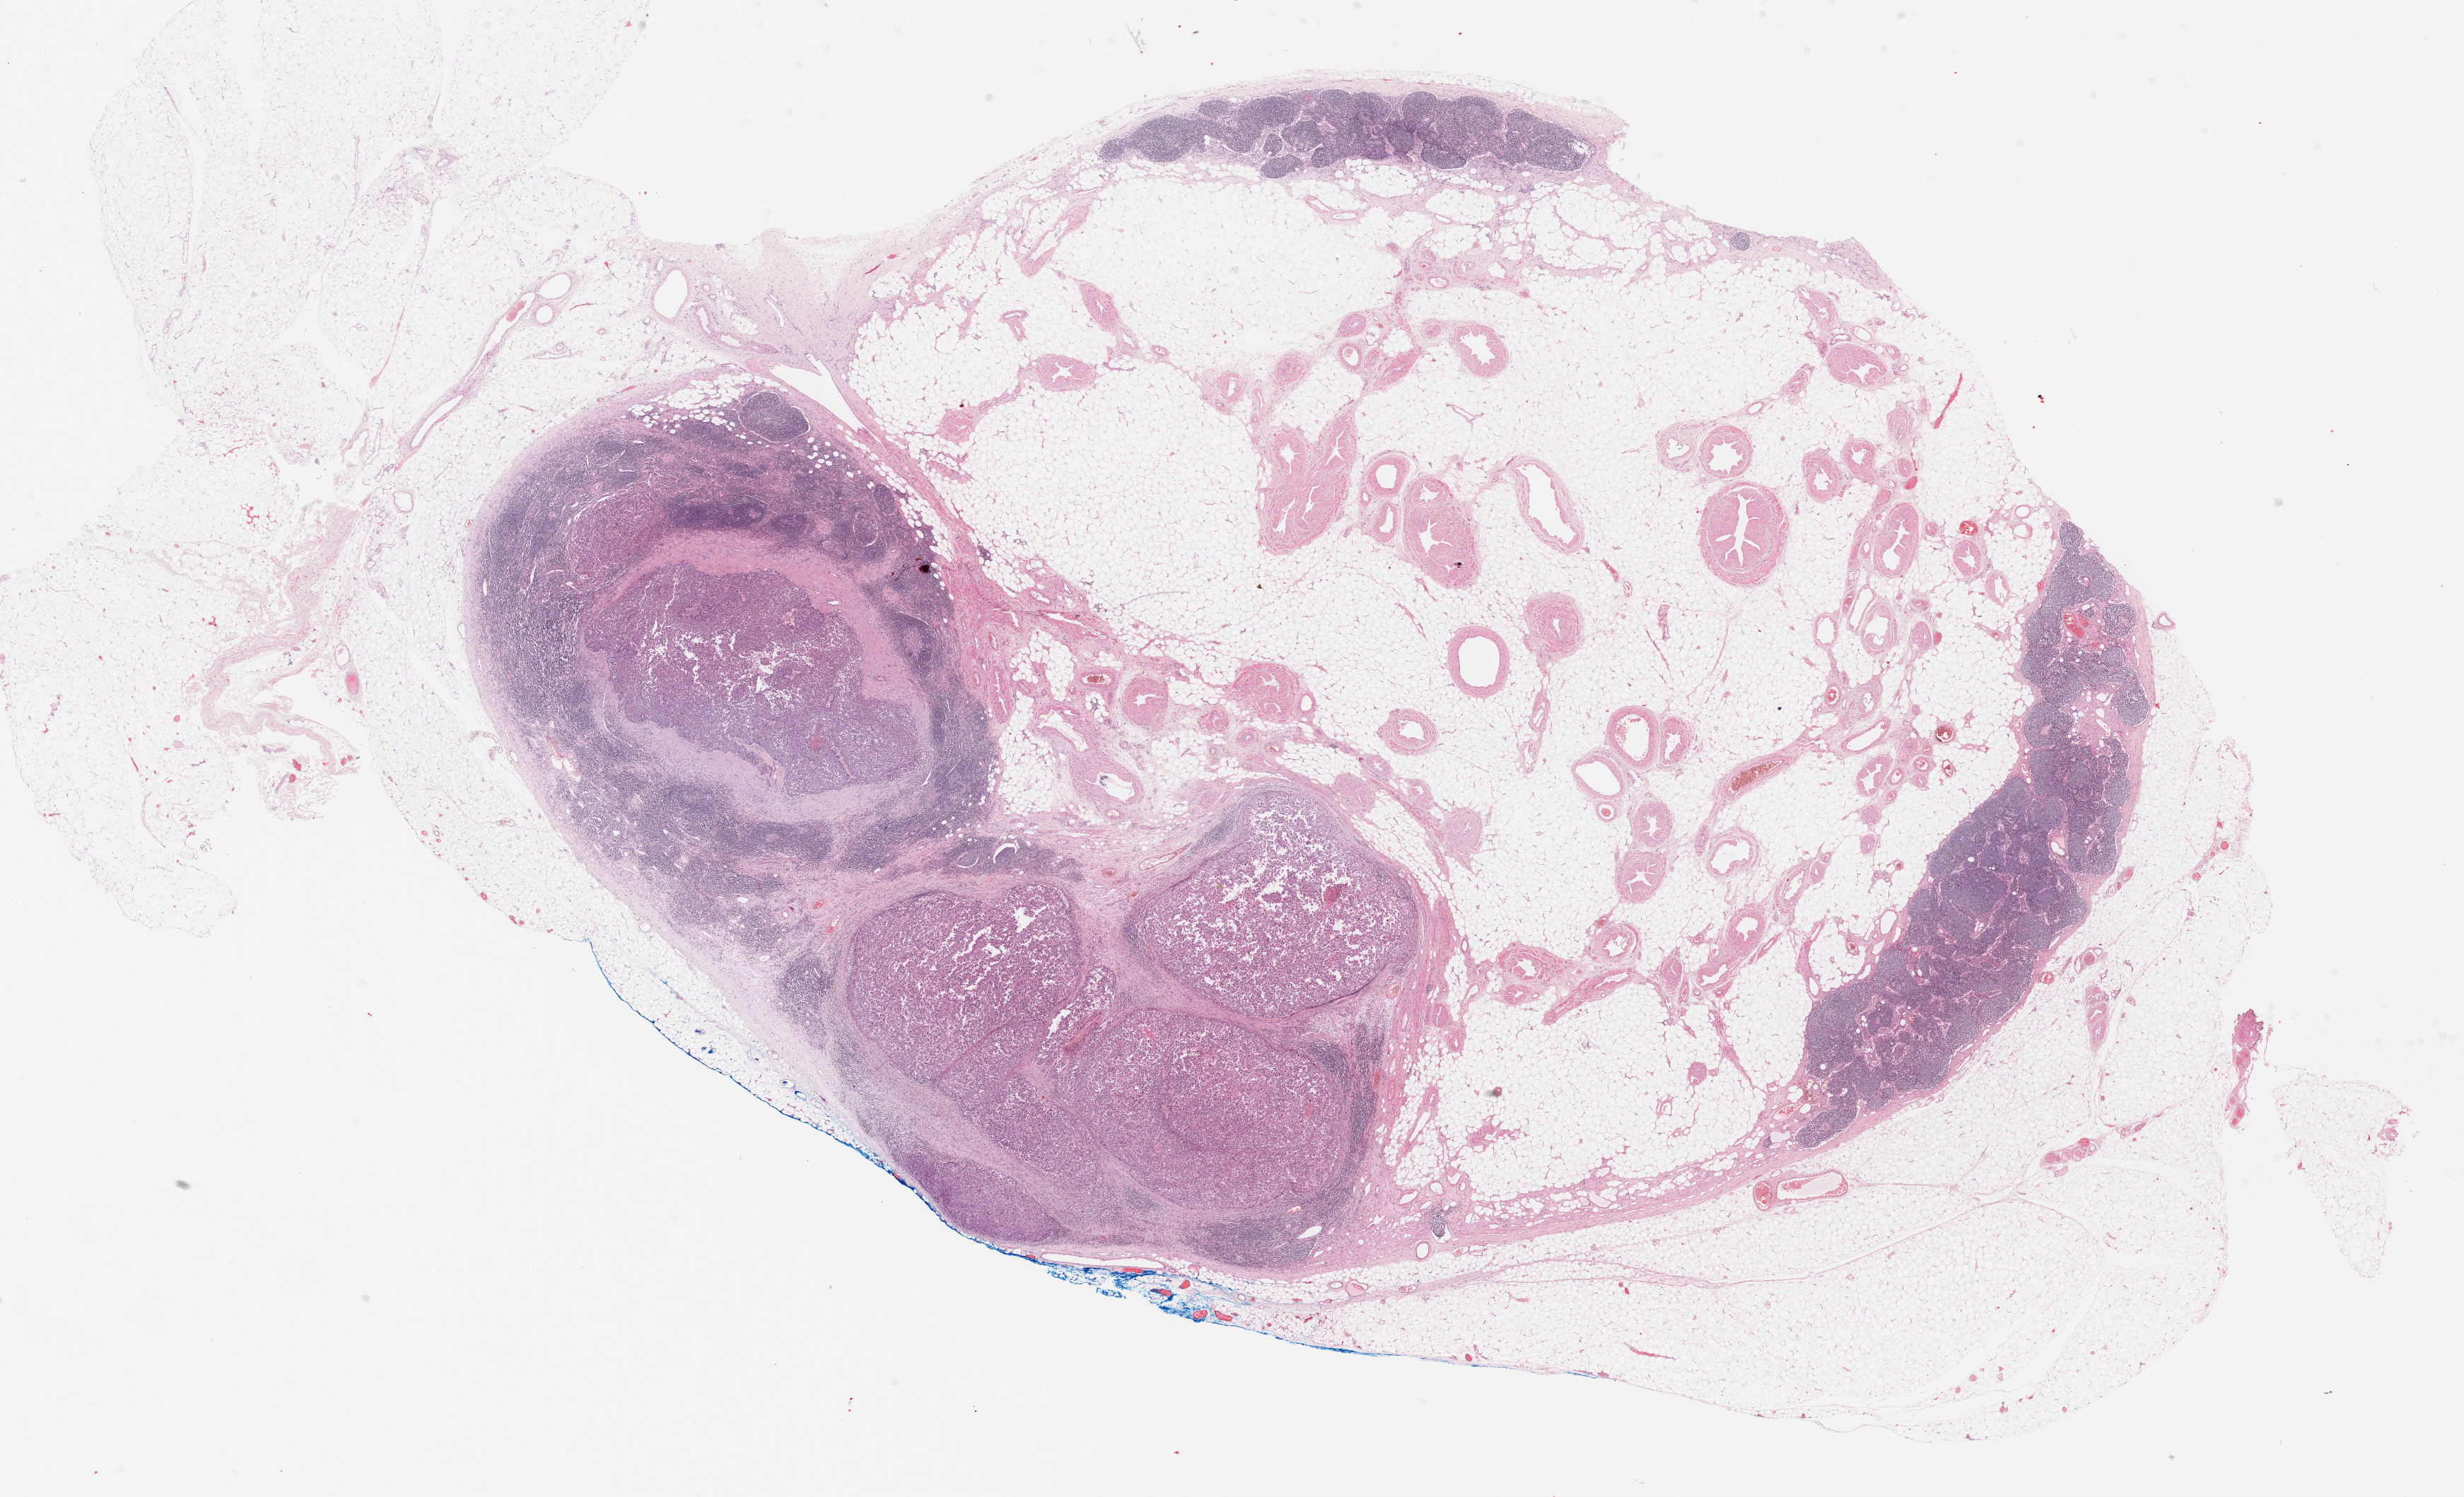
Whole-slide histology image, H&E-stained, whole scanned area (about 28.2 x 17.1 mm, slide scanned at 40x) shown as a low-resolution overview, formalin-fixed paraffin-embedded (FFPE) diagnostic section, metastatic tumour sample, sampled site: lymph nodes of inguinal region or leg. Male patient; age at initial diagnosis 70 years.
This section: metastatic tumour tissue. Patient diagnosis: Nodular melanoma.